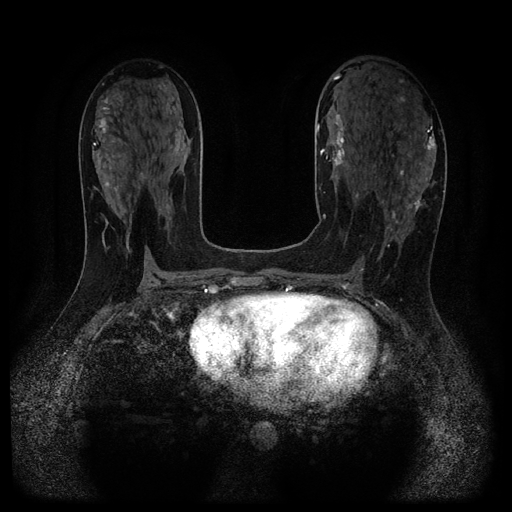
Breast MRI (dynamic contrast-enhanced, multi-phase), one axial slice; slice 56 of 116 in the series (ordered by position); dynamic contrast-enhanced series, time point 2 of 5 at this slice position (early post-contrast); 1.5 T; TE 2.7 ms, TR 5.4 ms; 2.2 mm slice thickness; 512 × 512 image matrix, field of view 330 × 330 mm. Female patient, age 43 years.
Annotated regions visible in this slice (semi-automatically segmented with operator editing):
- breast lesion (labelled 'tumour' in the annotation; benign lesions carry a separate 'benign' label): bounding box (x1, y1, x2, y2) in pixels: (410, 195, 425, 212)
- breast lesion (labelled benign in the annotation): (324, 108, 347, 171)